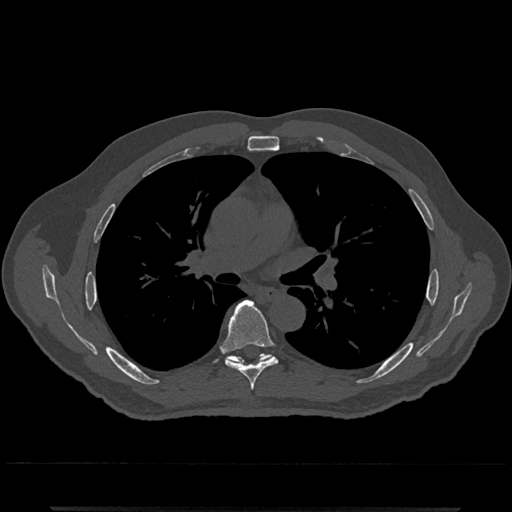
CT including the spine, one axial slice; slice 763 of 797 in the series (ordered by position); 120 kVp; bone window (W 1800 / L 400 HU); 0.5 mm slice thickness; 512 × 512 image matrix, field of view 393 × 393 mm. Patient: male, 67 years. Case-level facts recorded for this patient, not image findings: primary cancer: prostate.
Outlined on this slice (semi-automatic segmentation, software-assisted and operator-edited):
- T6 vertebra: bounding box [x1, y1, x2, y2] px = [221, 300, 278, 391]
- T7 vertebra: [227, 354, 271, 364]